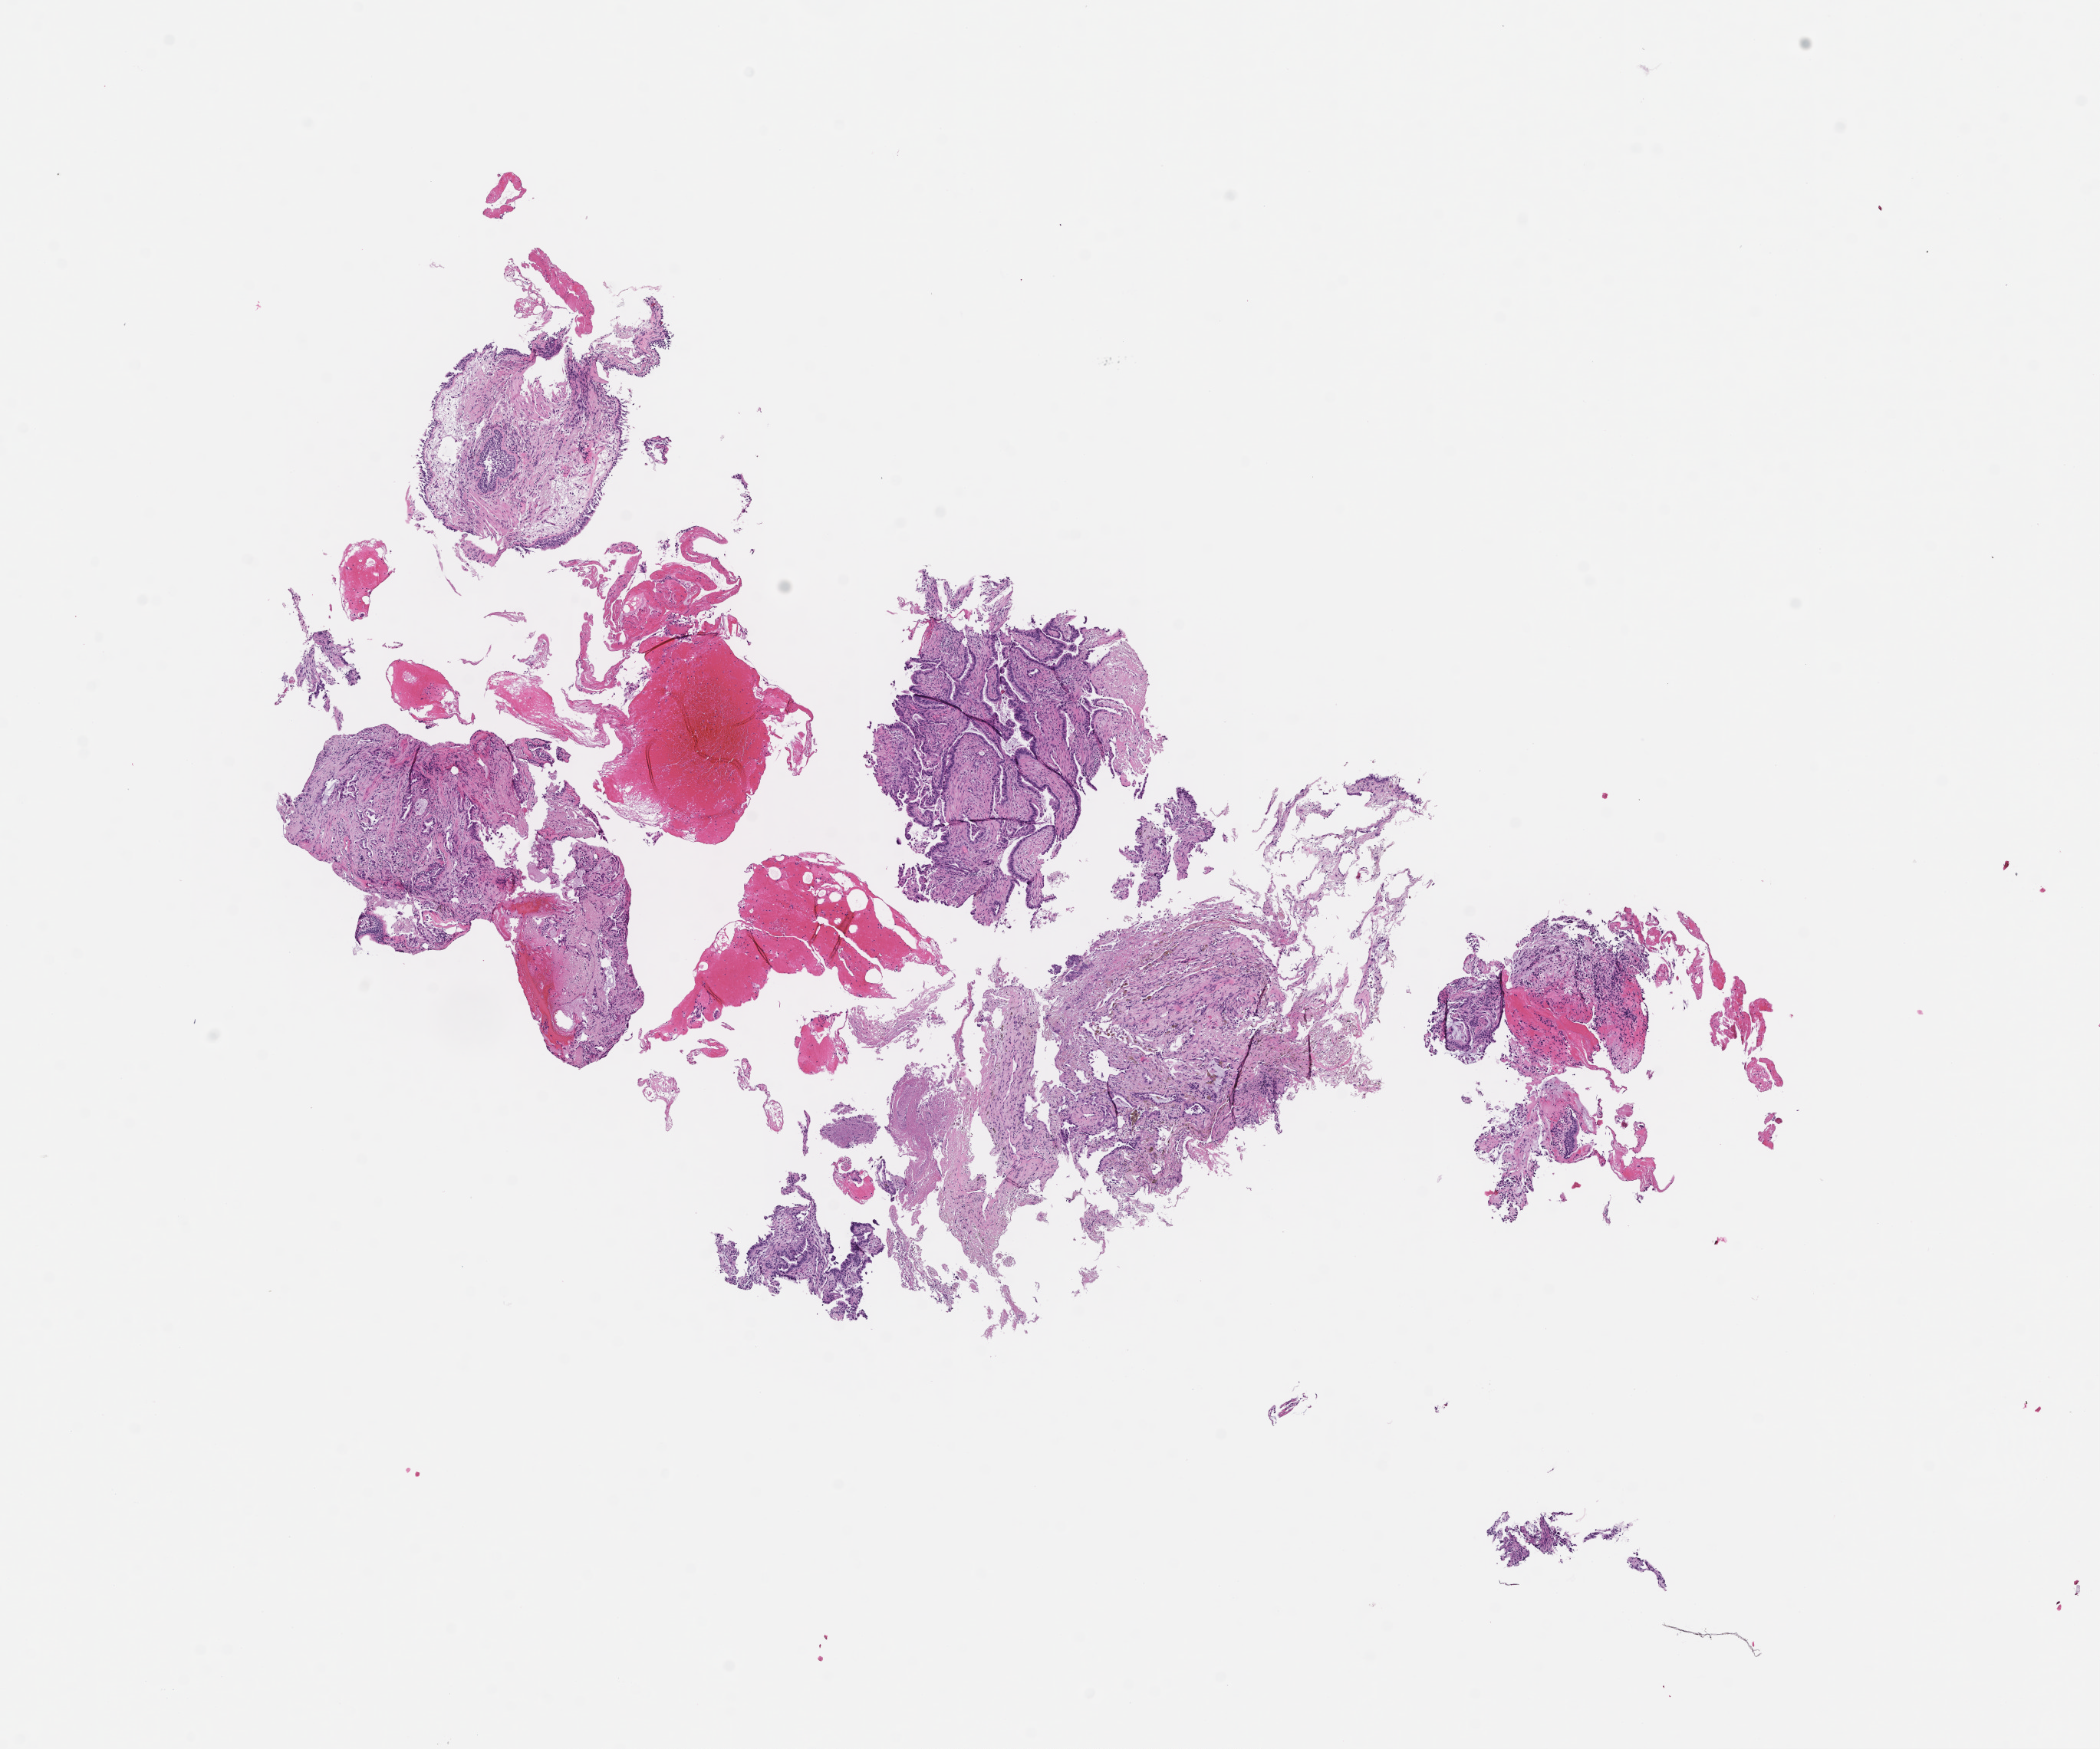
Hematoxylin and eosin (H&E) whole-slide image — low-resolution overview of the scanned area, about 11.1 x 9.2 mm, FFPE section, site: lung, specimen time point: archival tissue. Male patient.
This section: primary tumor. Diagnosis: Non-Small Cell Lung Carcinoma.